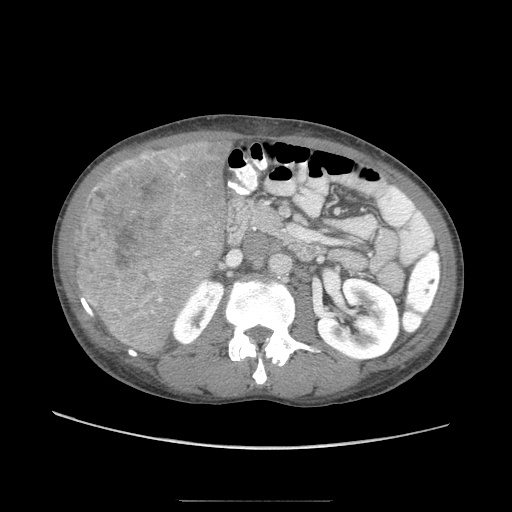
Contrast-enhanced abdominal CT (liver protocol), one axial slice; position 26 of 103 along the scan axis; soft-tissue window (W 400 / L 40 HU); 2.5 mm slice thickness; 512 × 512 image matrix. From the clinical record (not read from this slice): diagnosis: hepatocellular carcinoma (patient treated with transarterial chemoembolisation; whether this scan precedes or follows treatment is not stated here); TNM stage (as recorded): Stage-IIIA; Child-Pugh class: A; tumour size: 16 cm.
Structures marked on this image (semi-automatically segmented with operator editing):
- liver parenchyma outside the tumour (the mass and vessels are separate outlines, so this box may not span the whole liver): bounding box [x1, y1, x2, y2] px = [91, 132, 235, 354]
- mass: [71, 150, 210, 330]
- liver vessels: [152, 151, 167, 161]